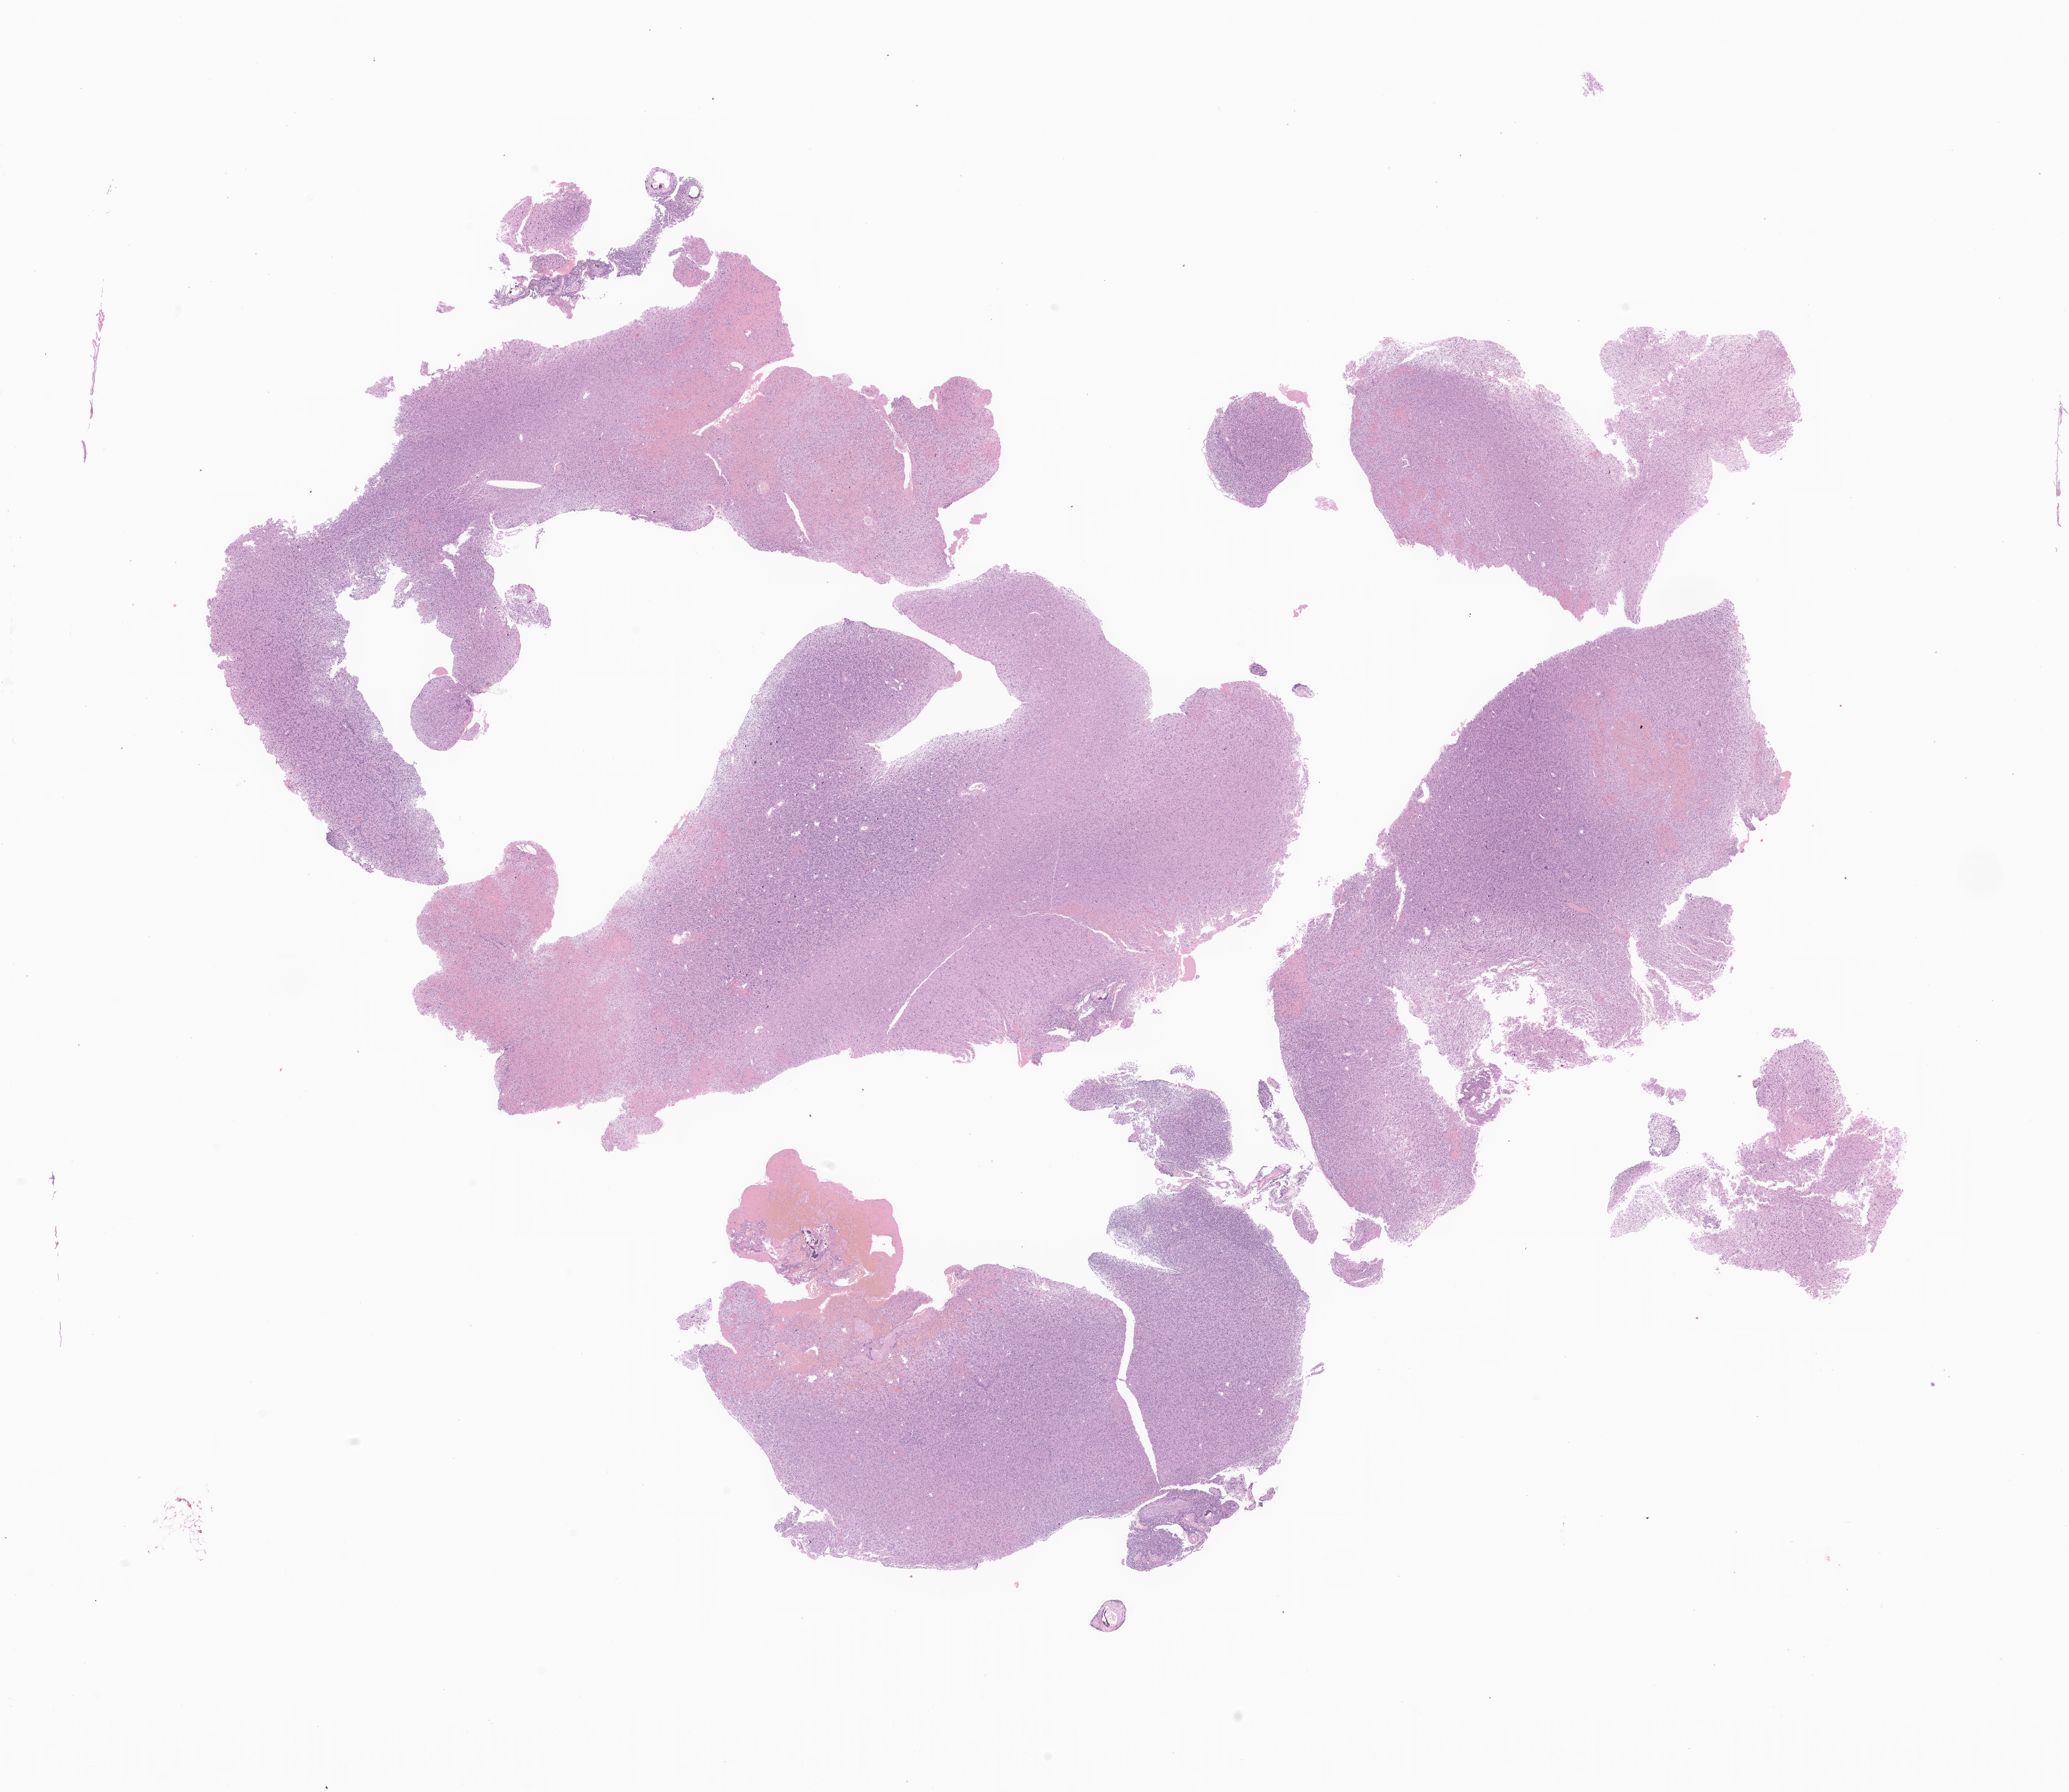
Whole-slide image, haematoxylin and eosin stain of tumor tissue from the brain — a low-resolution overview of the entire scanned area, about 23.7 x 20.5 mm. Formalin-fixed, paraffin-embedded (FFPE) tissue. Patient: male, age 212 months (17 years 8 months).
* recorded diagnosis: Astrocytoma, NOS